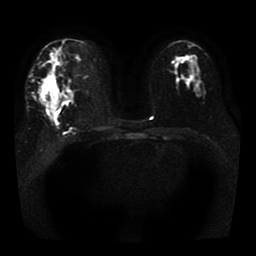
Breast MRI, one axial slice. Position 22 of 41 along the scan axis. Diffusion-weighted series; image 2 of 4 stored at this slice position (different b-values; order by instance number). 1.5 T. 5 mm slice thickness. 256 × 256 image matrix, field of view 330 × 330 mm. Female patient.
Outlined on this slice (outlined manually by an expert reader):
- tumour on diffusion-weighted imaging: bounding box <39,80,56,110> (left, top, right, bottom; pixels)